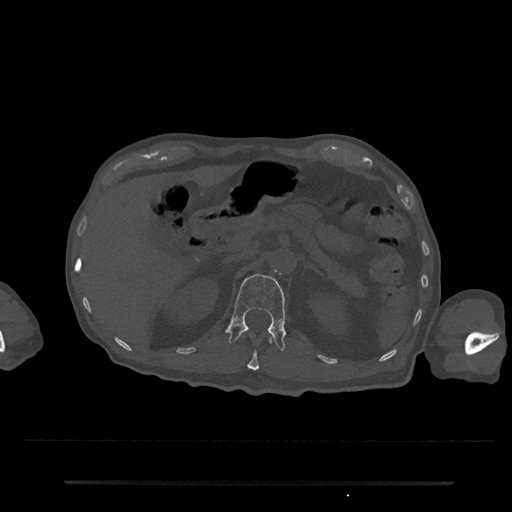
CT including the spine, one axial slice. Slice 150 of 797 in the series (ordered by position). Reconstruction kernel Br40s/3. 120 kVp. Bone window (W 1800 / L 400 HU). 0.5 mm slice thickness. 512 × 512 image matrix, field of view 427 × 427 mm. Patient: male, 74 years. From the clinical record (not read from this slice): primary cancer: prostate.
Annotated regions visible in this slice (semi-automatic segmentation, software-assisted and operator-edited):
- L1 vertebra: bounding box (x1, y1, x2, y2) in pixels: (226, 274, 286, 353)
- T12 vertebra: (243, 337, 272, 371)